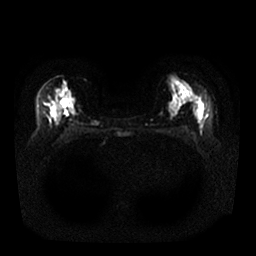
Breast MRI, one axial slice. Slice 13 of 25 in the series (ordered by position). Diffusion-weighted series; image 2 of 4 stored at this slice position (different b-values; order by instance number). 1.5 T. 256 × 256 image matrix, field of view 340 × 340 mm. Female patient.
Structures marked on this image (expert manual segmentation):
- tumour on diffusion-weighted imaging: box from (x=52, y=109) to (x=56, y=118) px